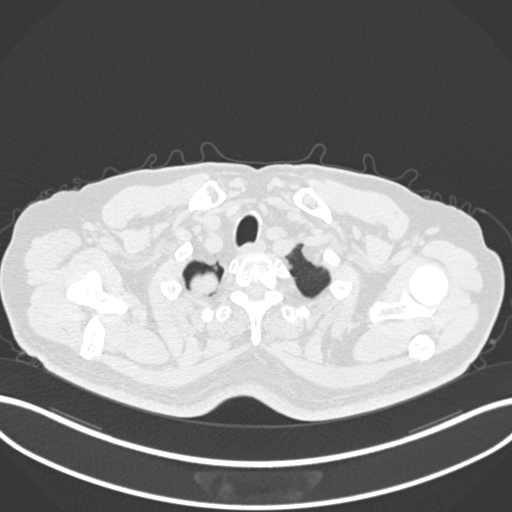
Chest CT, one axial slice; position 203 of 218 along the scan axis; reconstruction kernel B30f; lung window (W 1500 / L -600 HU); 1 mm slice thickness; 512 × 512 image matrix. Male patient, age 68 years. From the clinical record (not read from this slice): clinical TNM (as recorded): T2a N0 M0.
Structures marked on this image (bounding box drawn by a radiologist):
- lung tumour (recorded histology: adenocarcinoma): box from (x=186, y=270) to (x=223, y=302) px